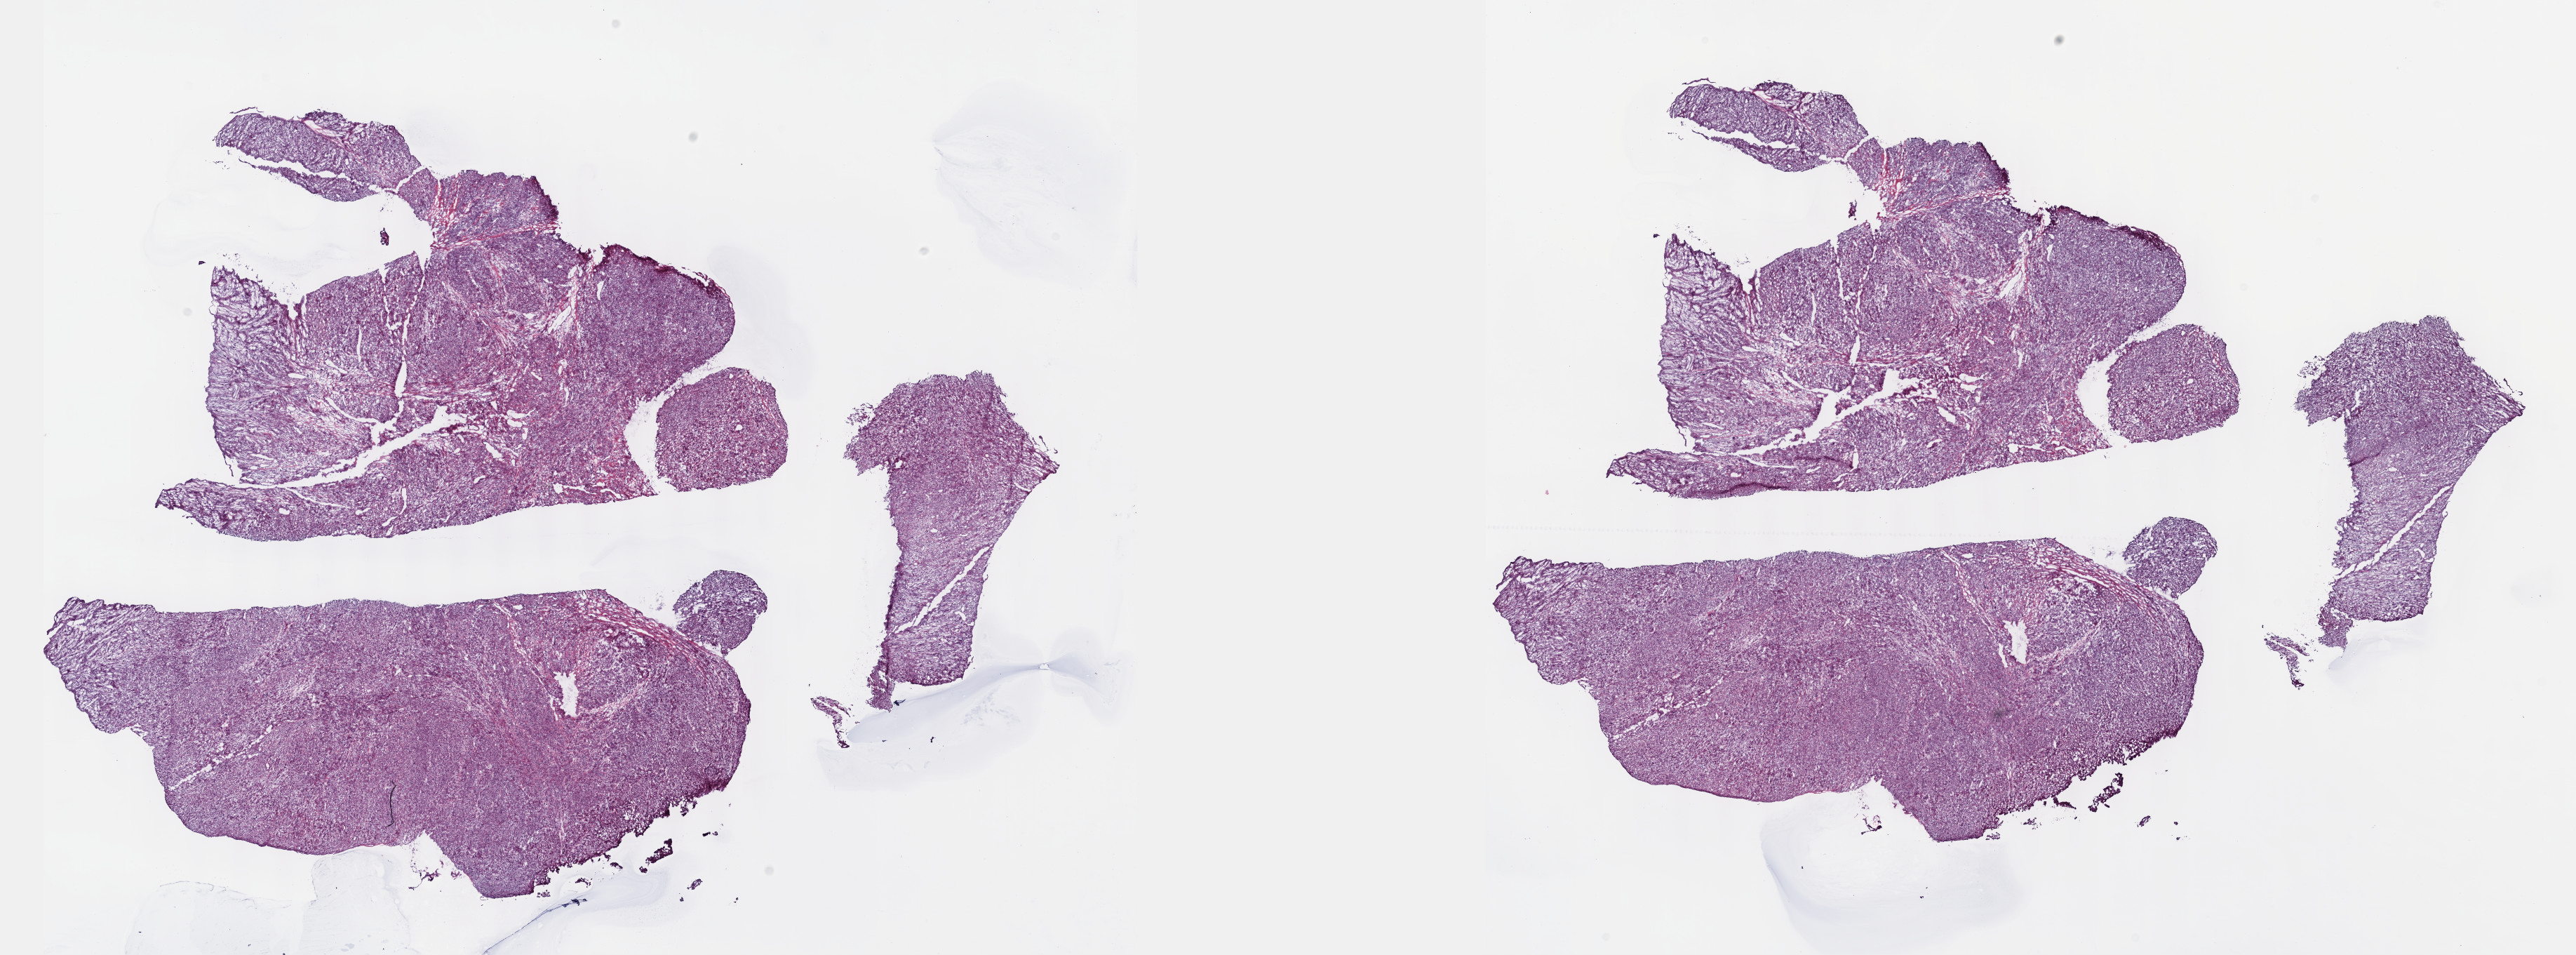
Whole-slide histology image, H&E, whole scanned area (about 29.7 x 11.0 mm) shown as a low-resolution overview; frozen section from the top of the tissue portion; primary tumour sample from the connective, subcutaneous and other soft tissues. Male, age 49 years at initial diagnosis. Composition of this section per pathologist review: tumour cells 100%, tumour nuclei 80%, normal cells 0%, stromal cells 0%, necrosis 0%. Inflammatory infiltration, as recorded: lymphocyte infiltration 1%, monocyte infiltration 0%, neutrophil infiltration 0%.
Diagnosis: Leiomyosarcoma, NOS (connective, subcutaneous and other soft tissues of lower limb and hip).